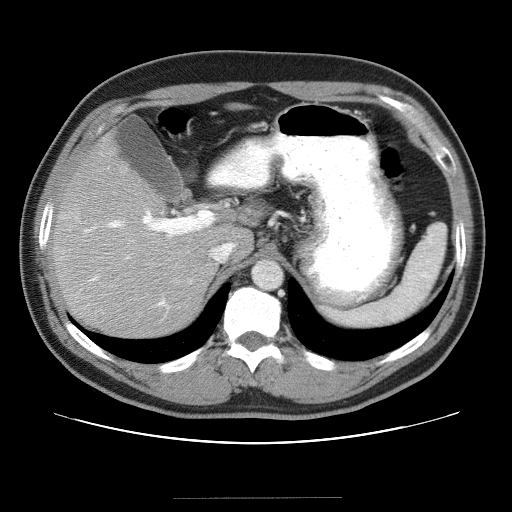
Contrast-enhanced abdominal CT (liver protocol), one axial slice; position 24 of 40 along the scan axis; reconstruction kernel STANDARD; 120 kVp; soft-tissue window (W 400 / L 40 HU); 5 mm slice thickness; 512 × 512 image matrix, field of view 380 × 380 mm. From the clinical record (not read from this slice): diagnosis: hepatocellular carcinoma (patient treated with transarterial chemoembolisation; whether this scan precedes or follows treatment is not stated here); TNM stage (as recorded): Stage-IVA.
Annotated regions visible in this slice (semi-automatically segmented with operator editing):
- liver parenchyma outside the tumour (the mass and vessels are separate outlines, so this box may not span the whole liver): bounding box [x1, y1, x2, y2] px = [50, 132, 257, 336]
- mass: [57, 202, 80, 228]
- liver vessels: [62, 210, 170, 309]